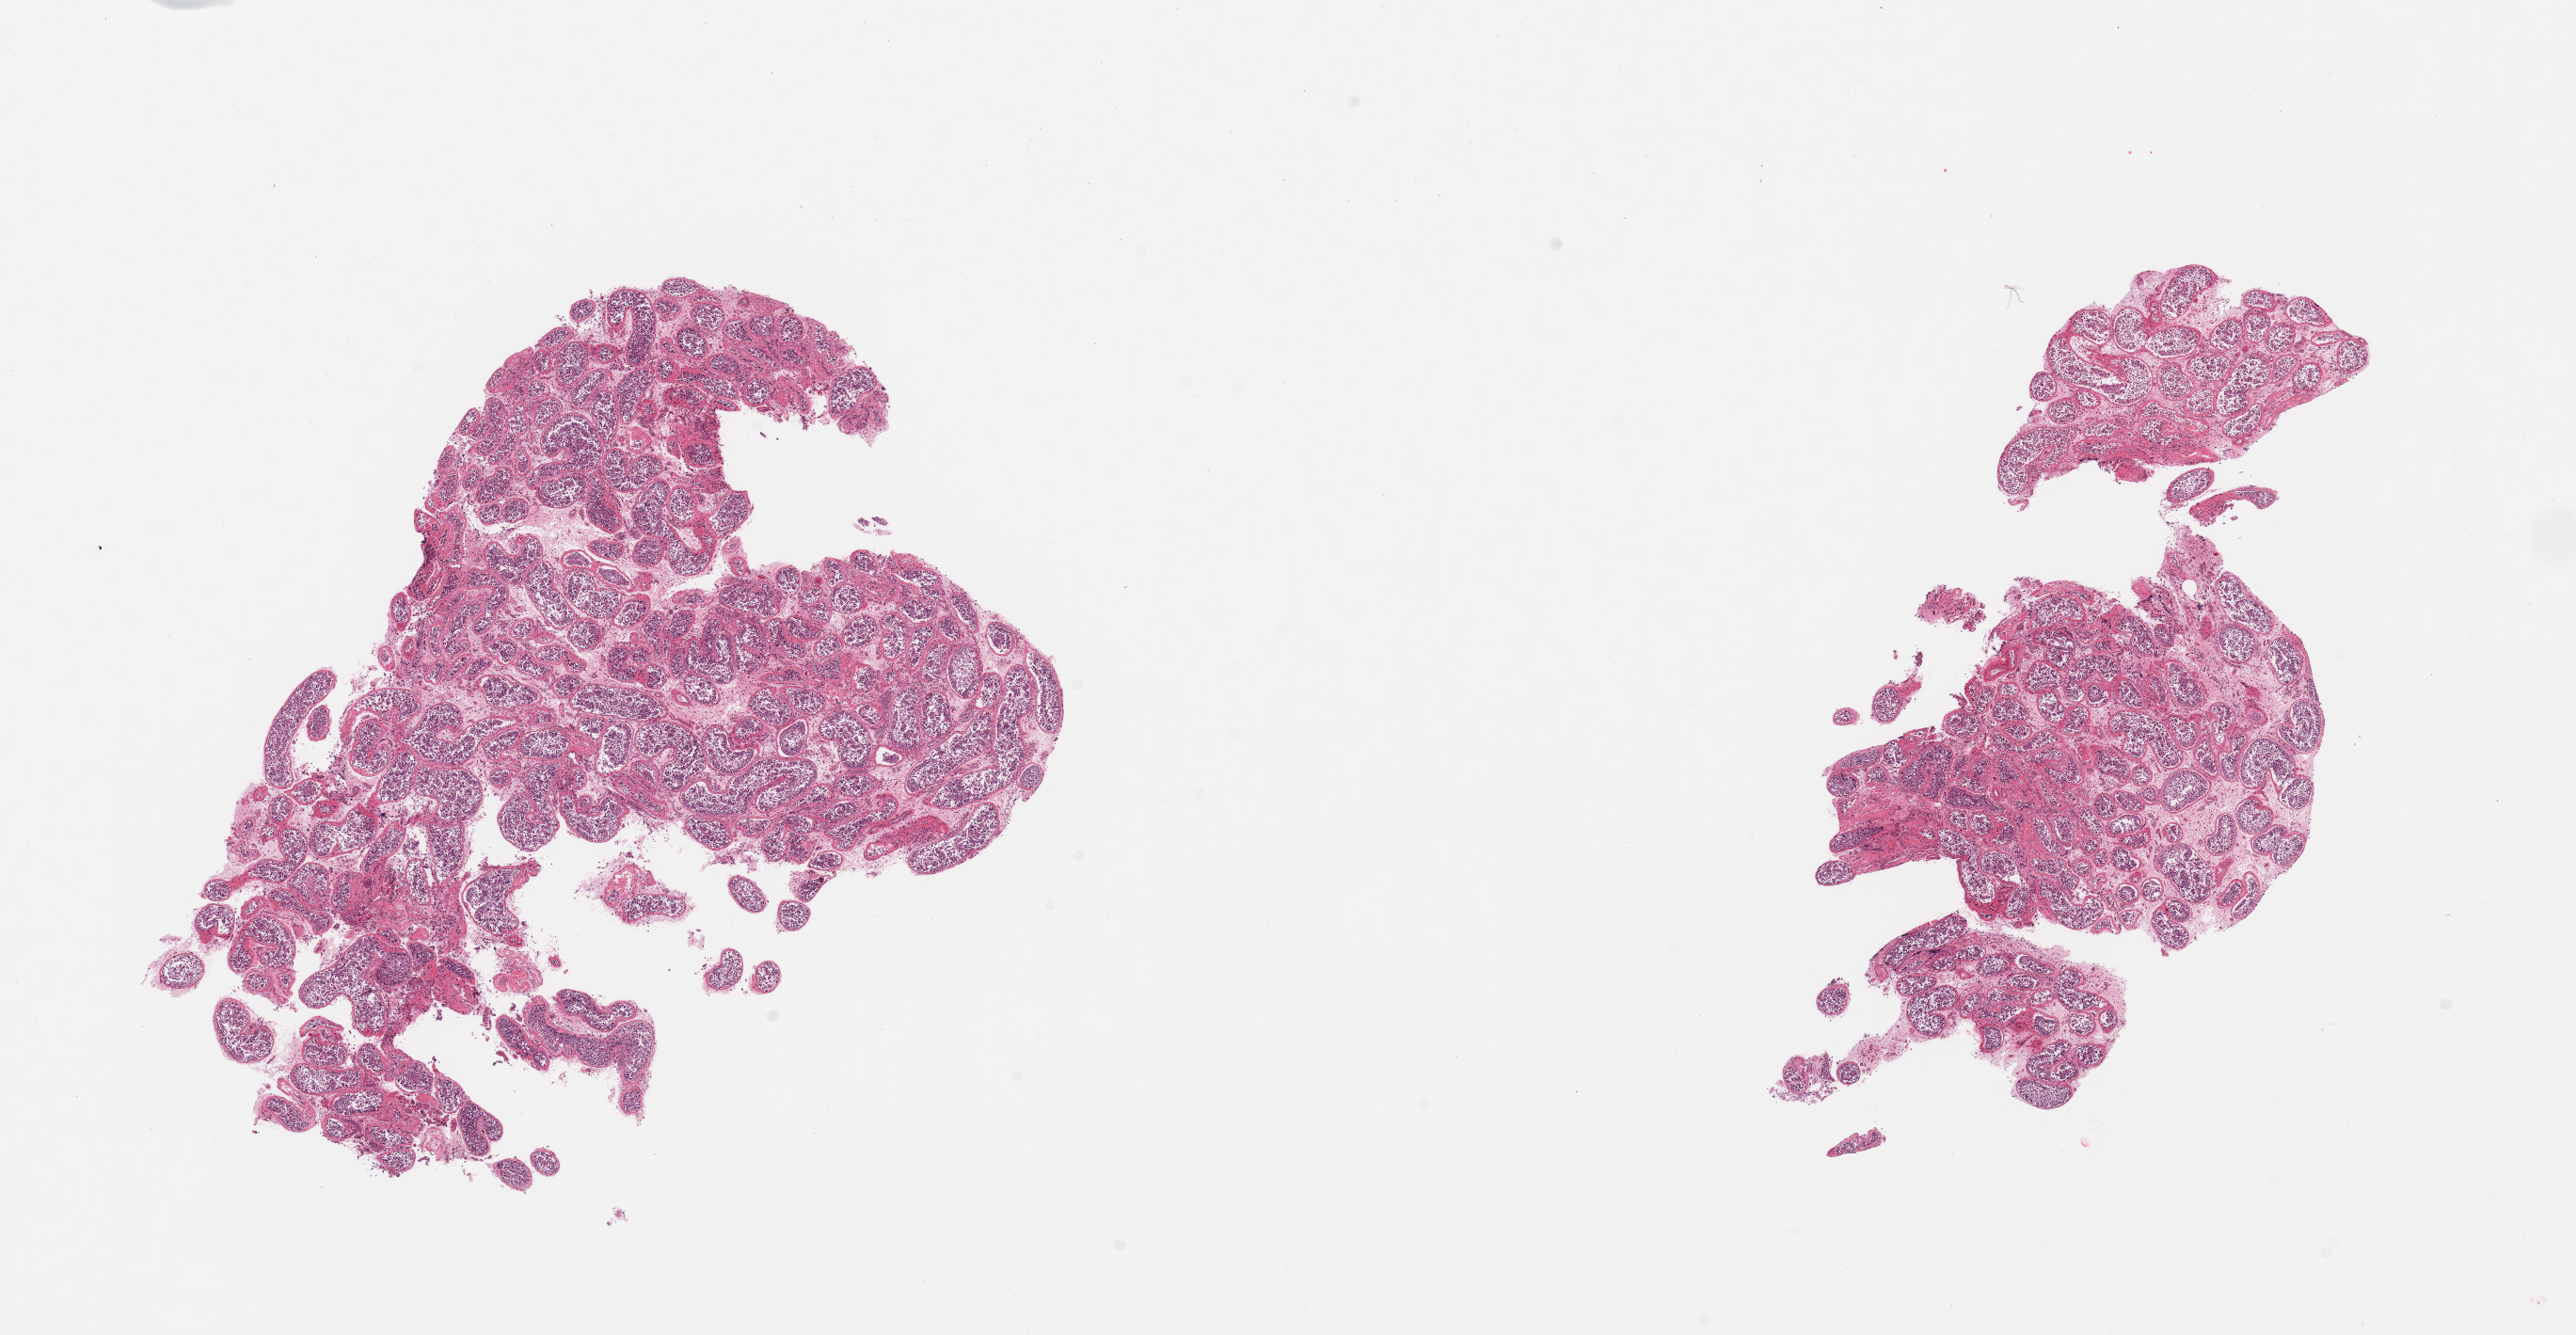
Digitized hematoxylin and eosin (H&E)-stained section, whole scanned area (about 21.7 x 11.2 mm, slide scanned at 20x) shown as a low-resolution overview; PAXgene-fixed paraffin-embedded (PFPE) section; section of testis (target tissue); donor tissue sample. Donor: male.
• pathologist's review note for this sample: 2 pieces; some increased peritubular fibrosis